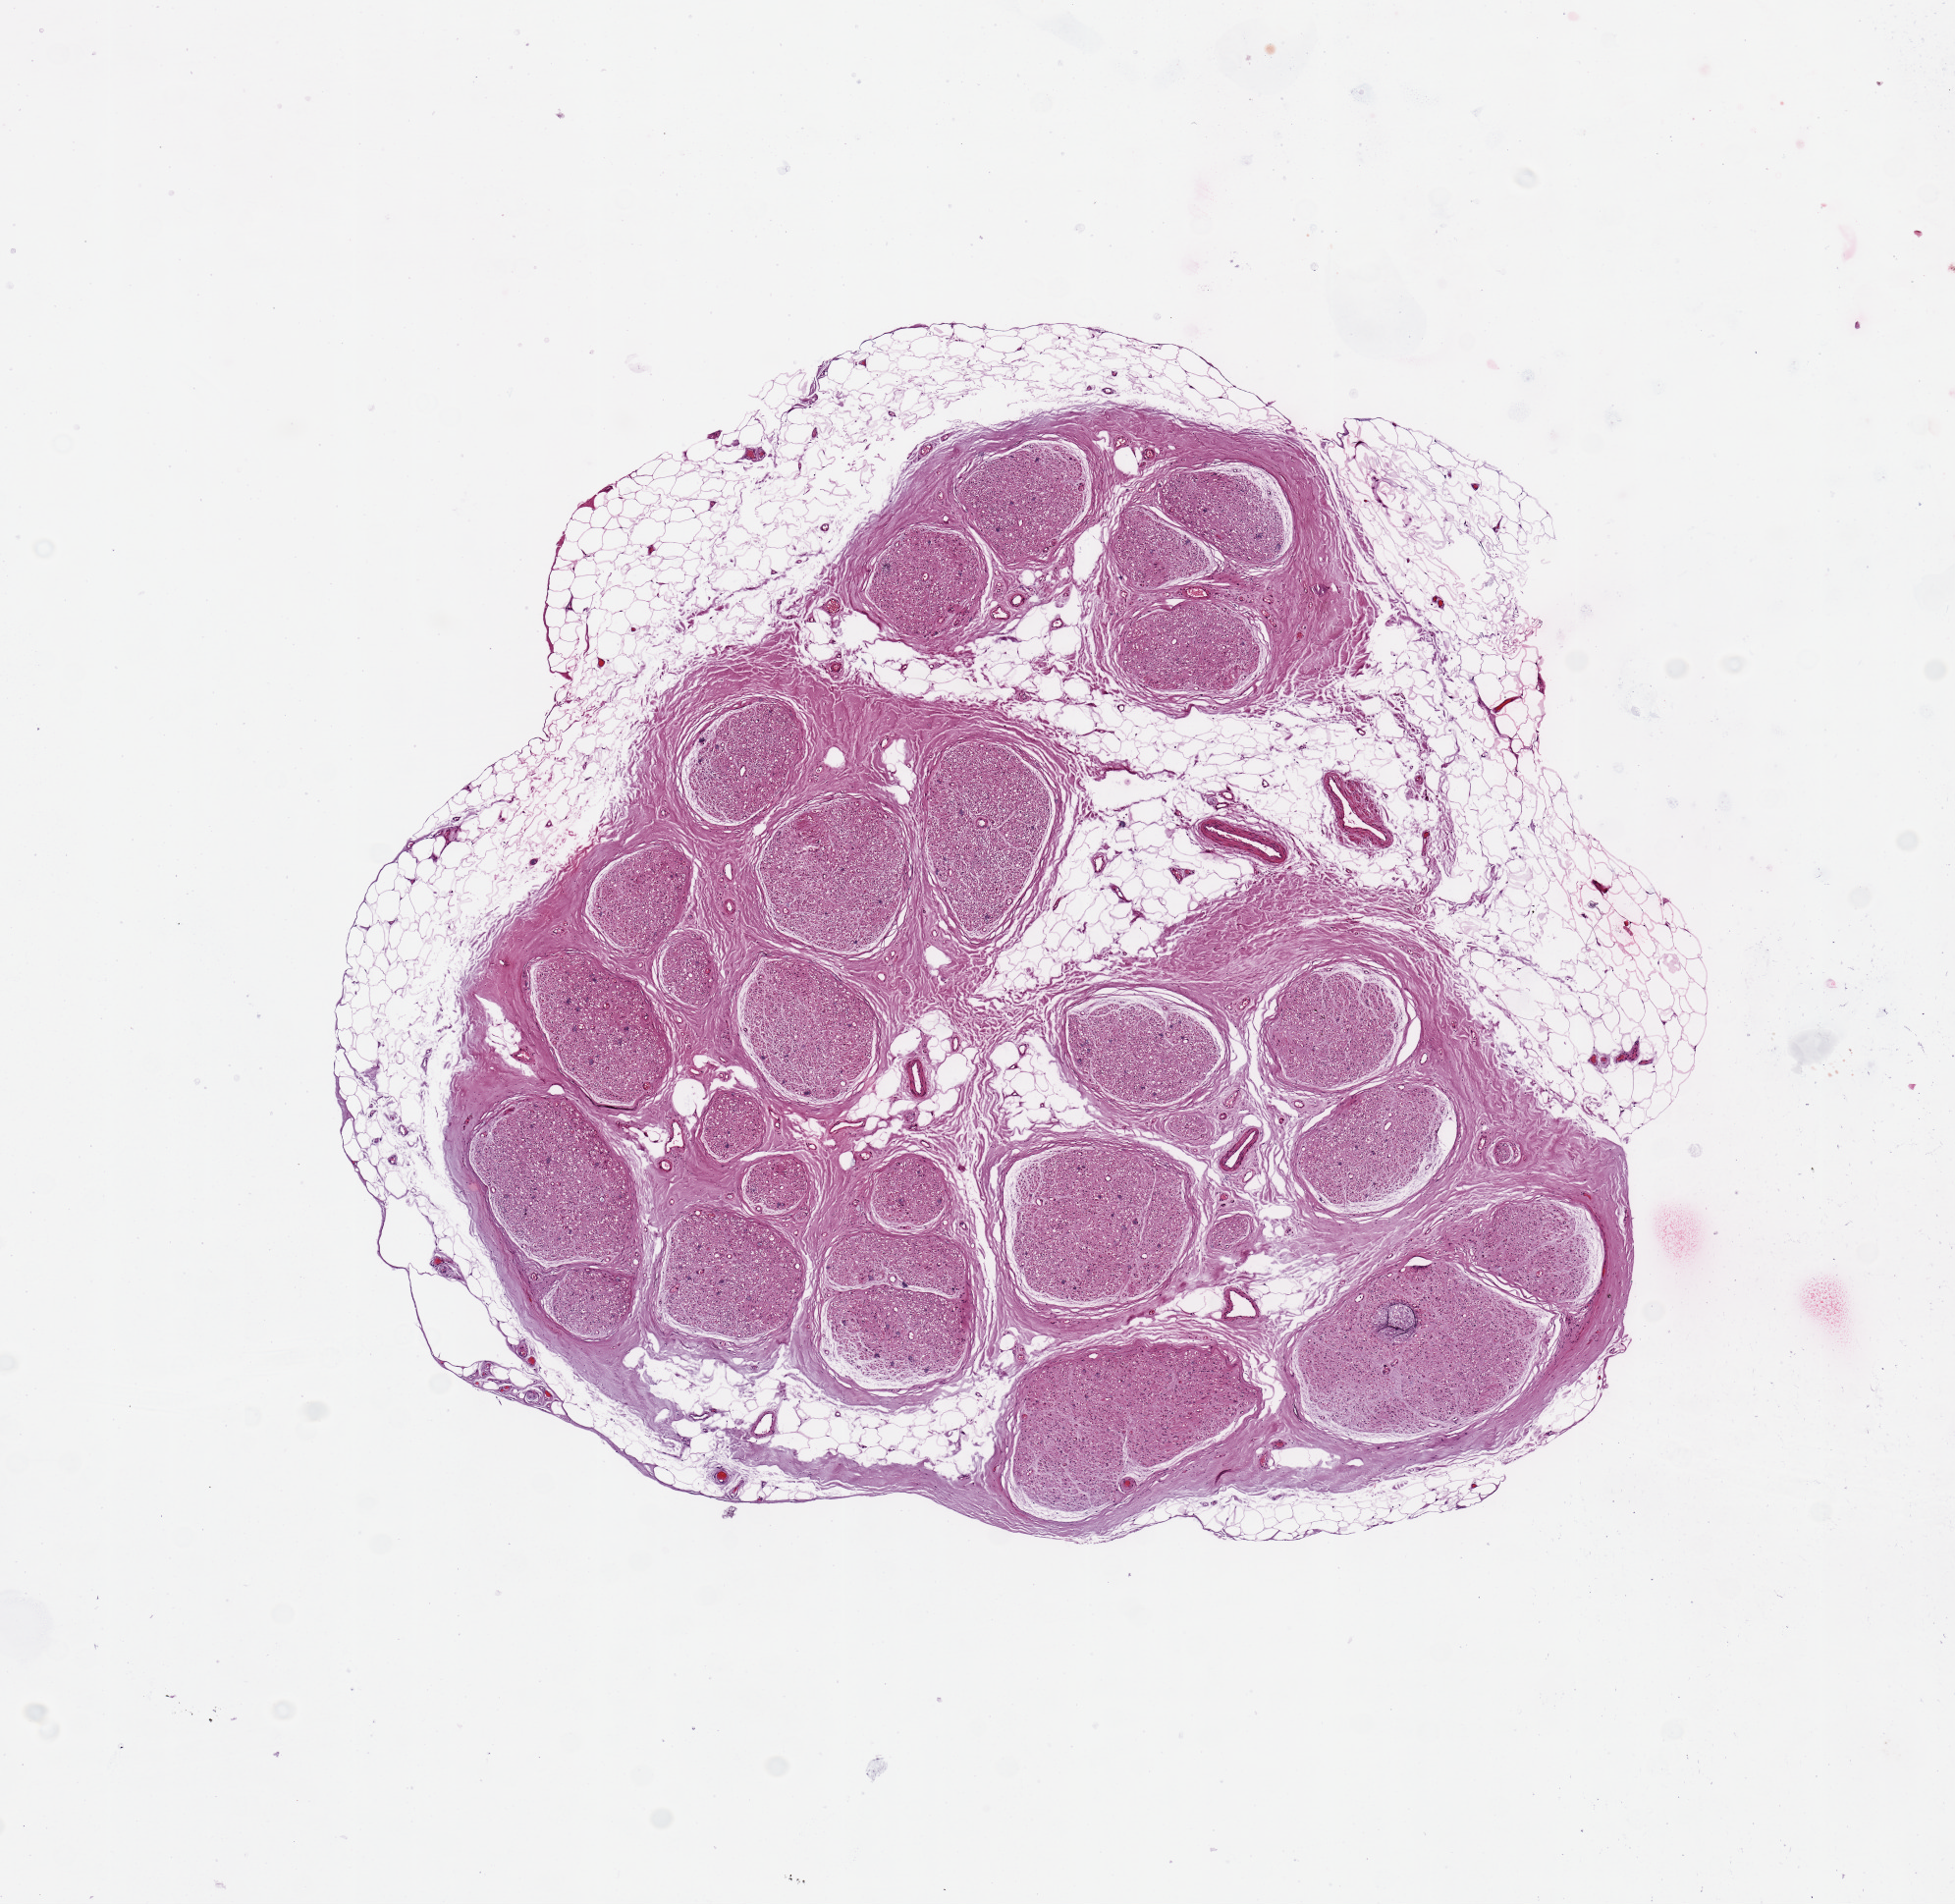
Whole-slide image, H&E stain, brightfield — shown as a low-resolution overview of the whole scanned area (about 7.9 x 7.7 mm). PAXgene-fixed, paraffin-embedded tissue. Section of tibial nerve (target tissue). Tissue donor sample. Donor: male.
• pathologist's review note for this sample: 4.5 mm x 4.5 mm